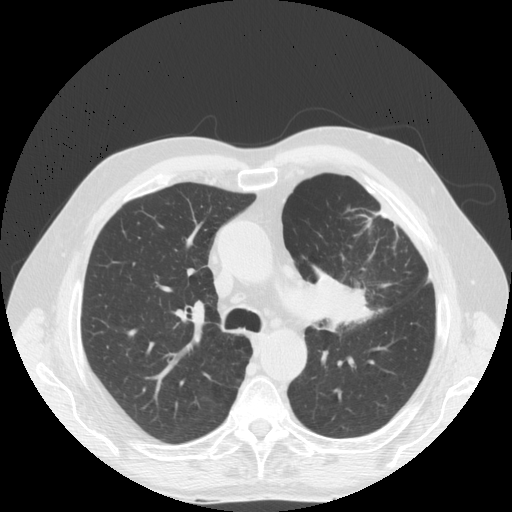
Low-dose screening chest CT, one axial slice. Slice 117 of 170 in the series (ordered by position). Reconstruction kernel STANDARD. 140 kVp. Lung window (W 1500 / L -600 HU). 2.5 mm slice thickness. 512 × 512 image matrix, field of view 380 × 380 mm.
Annotated regions visible in this slice (manually delineated by an expert):
- lesion 1 (tumor, upper lobe of left lung): bounding box [x1, y1, x2, y2] px = [305, 269, 382, 332]